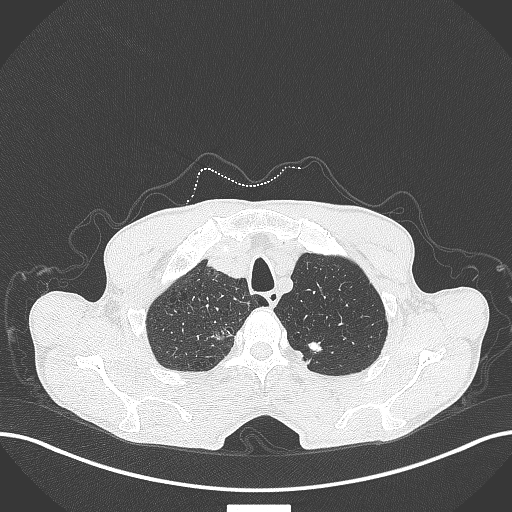
Chest CT, one axial slice. Position 377 of 445 along the scan axis. Reconstruction kernel B70f. 120 kVp. Lung window (W 1500 / L -600 HU). 1 mm slice thickness. 512 × 512 image matrix, field of view 400 × 400 mm. Male patient, age 70 years. From the clinical record (not read from this slice): clinical TNM (as recorded): T1a N0 M0; histopathological grade: G1-2.
Structures marked on this image (bounding box drawn by a radiologist):
- lung tumour (recorded histology: adenocarcinoma): box from (x=208, y=318) to (x=240, y=346) px